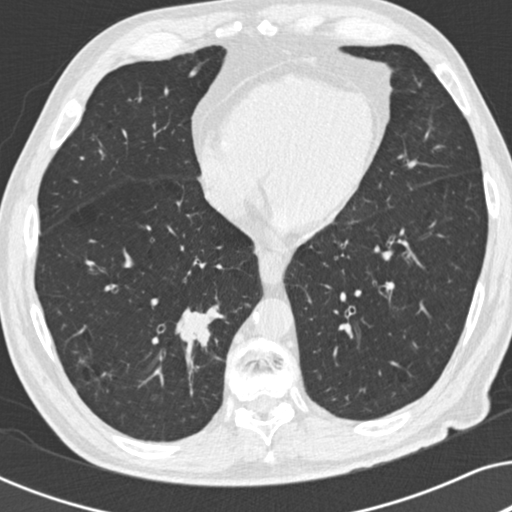
Low-dose screening chest CT, one axial slice; slice 82 of 191 in the series (ordered by position); 120 kVp; lung window (W 1500 / L -600 HU); 2 mm slice thickness; 512 × 512 image matrix, field of view 330 × 330 mm.
Annotated regions visible in this slice (outlined manually by an expert reader):
- lesion 1 (tumor, lower lobe of right lung): box from (x=179, y=305) to (x=217, y=344) px